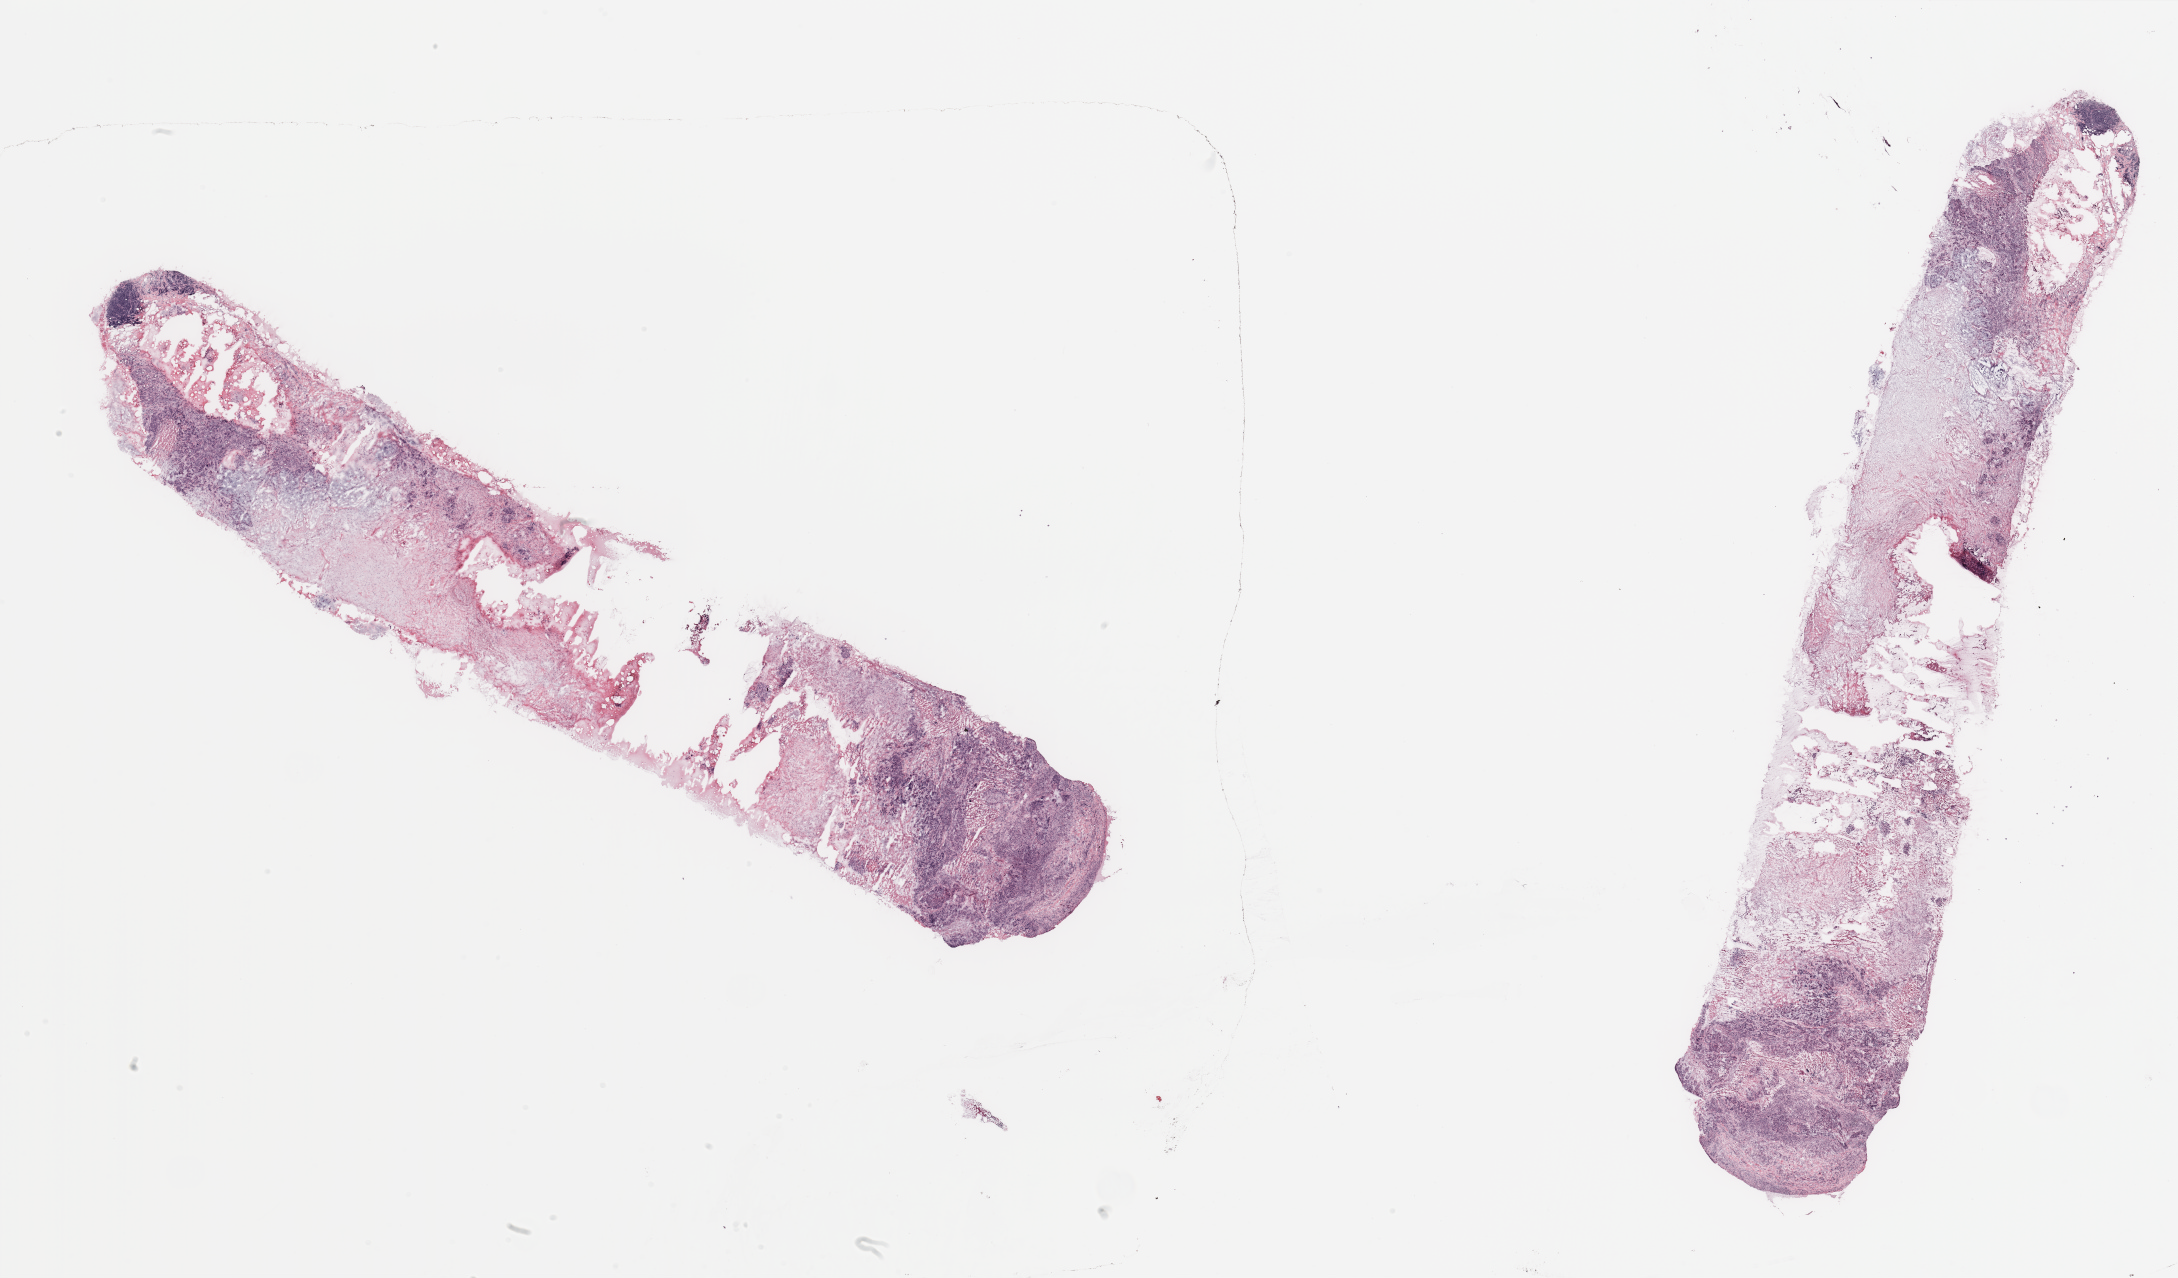
H&E-stained whole-slide image — whole scanned area (about 34.5 x 20.2 mm) shown as a low-resolution overview. 64-year-old female patient.
• specimen: breast, tumour tissue